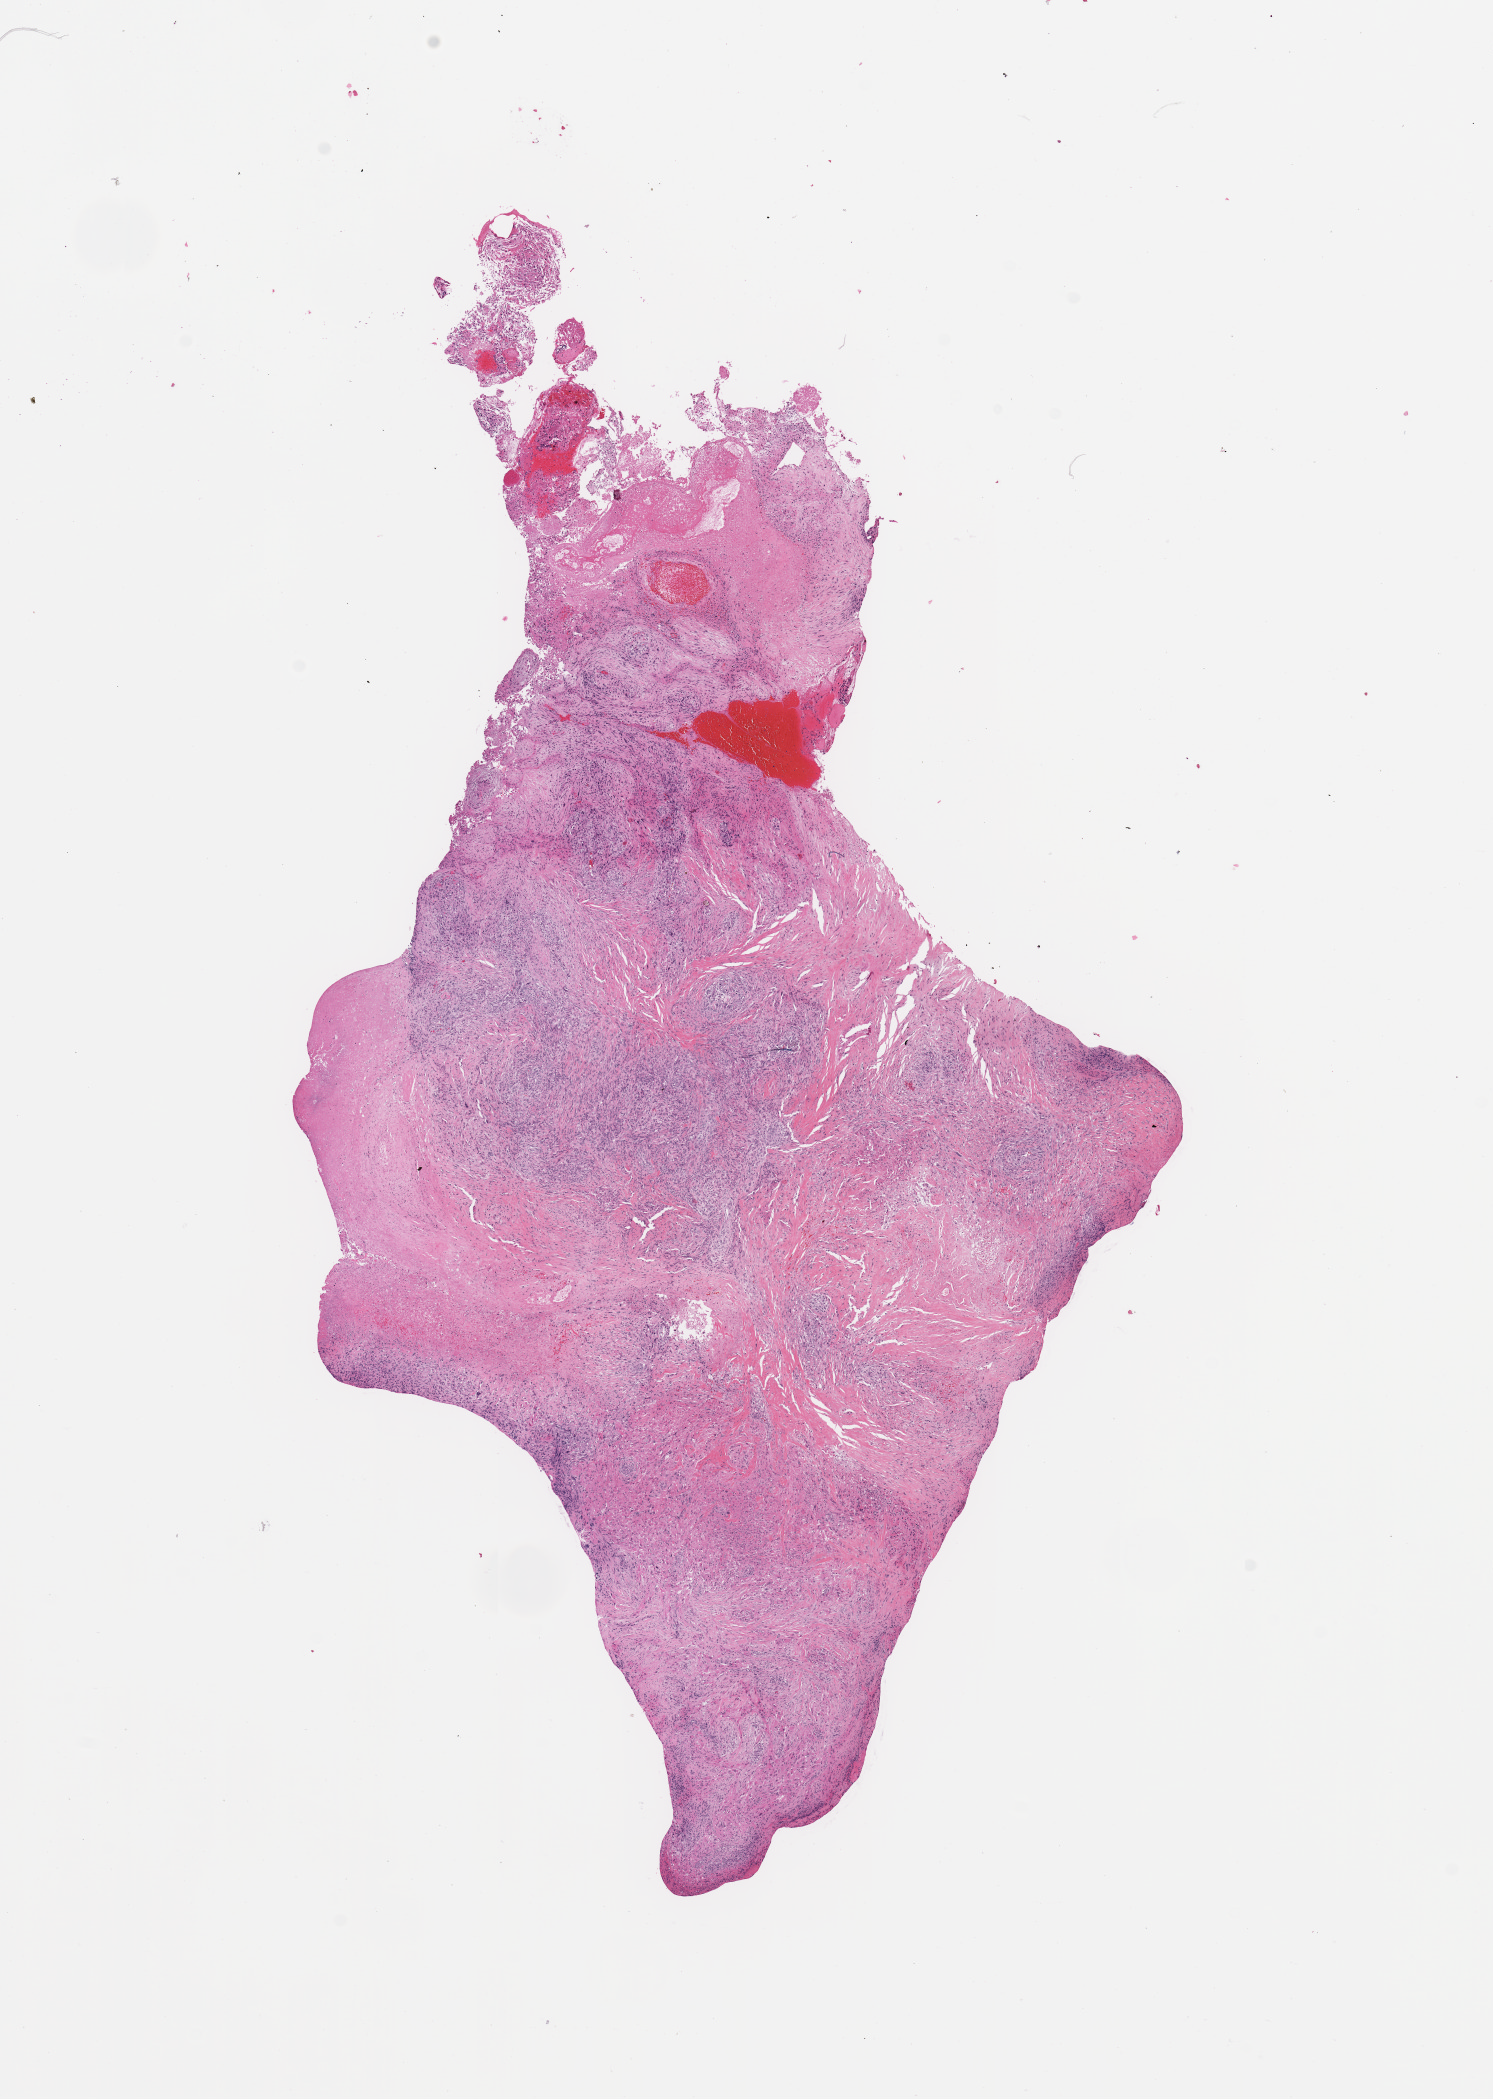
Digitized H&E-stained tissue section (whole slide) — whole scanned area (about 11.8 x 16.6 mm, acquisition: 20x scan) shown as a low-resolution overview. Tumour tissue sample, sampled site: frontal lobe. 46-year-old male patient. Composition of this section per pathologist review: tumour nuclei 65%, necrosis 30%.
• histologic diagnosis: Glioblastoma